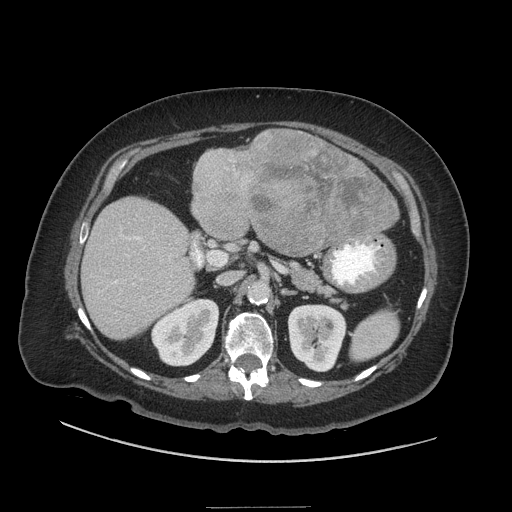
Contrast-enhanced abdominal CT (liver protocol), one axial slice; slice 17 of 81 in the series (ordered by position); reconstruction kernel STANDARD; soft-tissue window (W 400 / L 40 HU); 2.5 mm slice thickness; 512 × 512 image matrix, field of view 440 × 440 mm. Case-level facts recorded for this patient, not image findings: diagnosis: hepatocellular carcinoma (patient treated with transarterial chemoembolisation; whether this scan precedes or follows treatment is not stated here); TNM stage (as recorded): Stage-II; Child-Pugh class: A; tumour differentiation: moderately differentiated; tumour nodularity: multinodular.
Outlined on this slice (semi-automatically segmented with operator editing):
- liver parenchyma outside the tumour (the mass and vessels are separate outlines, so this box may not span the whole liver): box from (x=82, y=138) to (x=388, y=338) px
- mass: (x=192, y=129)–(x=401, y=255)
- liver vessels: (x=112, y=229)–(x=172, y=296)